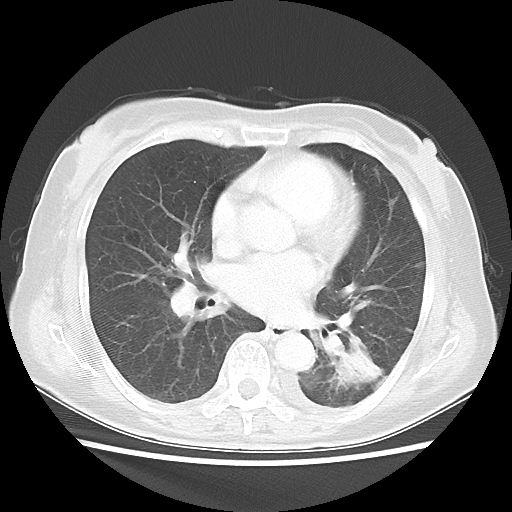
Chest CT, one axial slice. Slice 17 of 40 in the series (ordered by position). Reconstruction kernel LUNG. 100 kVp. Lung window (W 1500 / L -600 HU). 5 mm slice thickness. 512 × 512 image matrix, field of view 341 × 341 mm. Patient: female, 69 years. From the clinical record (not read from this slice): clinical TNM (as recorded): T1c N0 M0.
Structures marked on this image (rectangle marked by the reading radiologist):
- lung tumour (recorded histology: adenocarcinoma): bounding box <327,336,392,397> (left, top, right, bottom; pixels)